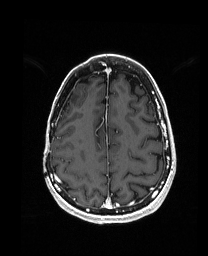
Brain MRI from a brain-tumour surgery series, one axial slice; T1-weighted post-contrast; 1 mm slice thickness; 208 × 256 image matrix. From the clinical record (not read from this slice): histopathology: Metastatic Carcinoma from Breast primary; tumour location: Right Frontal.
Annotated regions visible in this slice (expert manual segmentation):
- previous resection cavity: bounding box (x1, y1, x2, y2) in pixels: (66, 103, 68, 106)